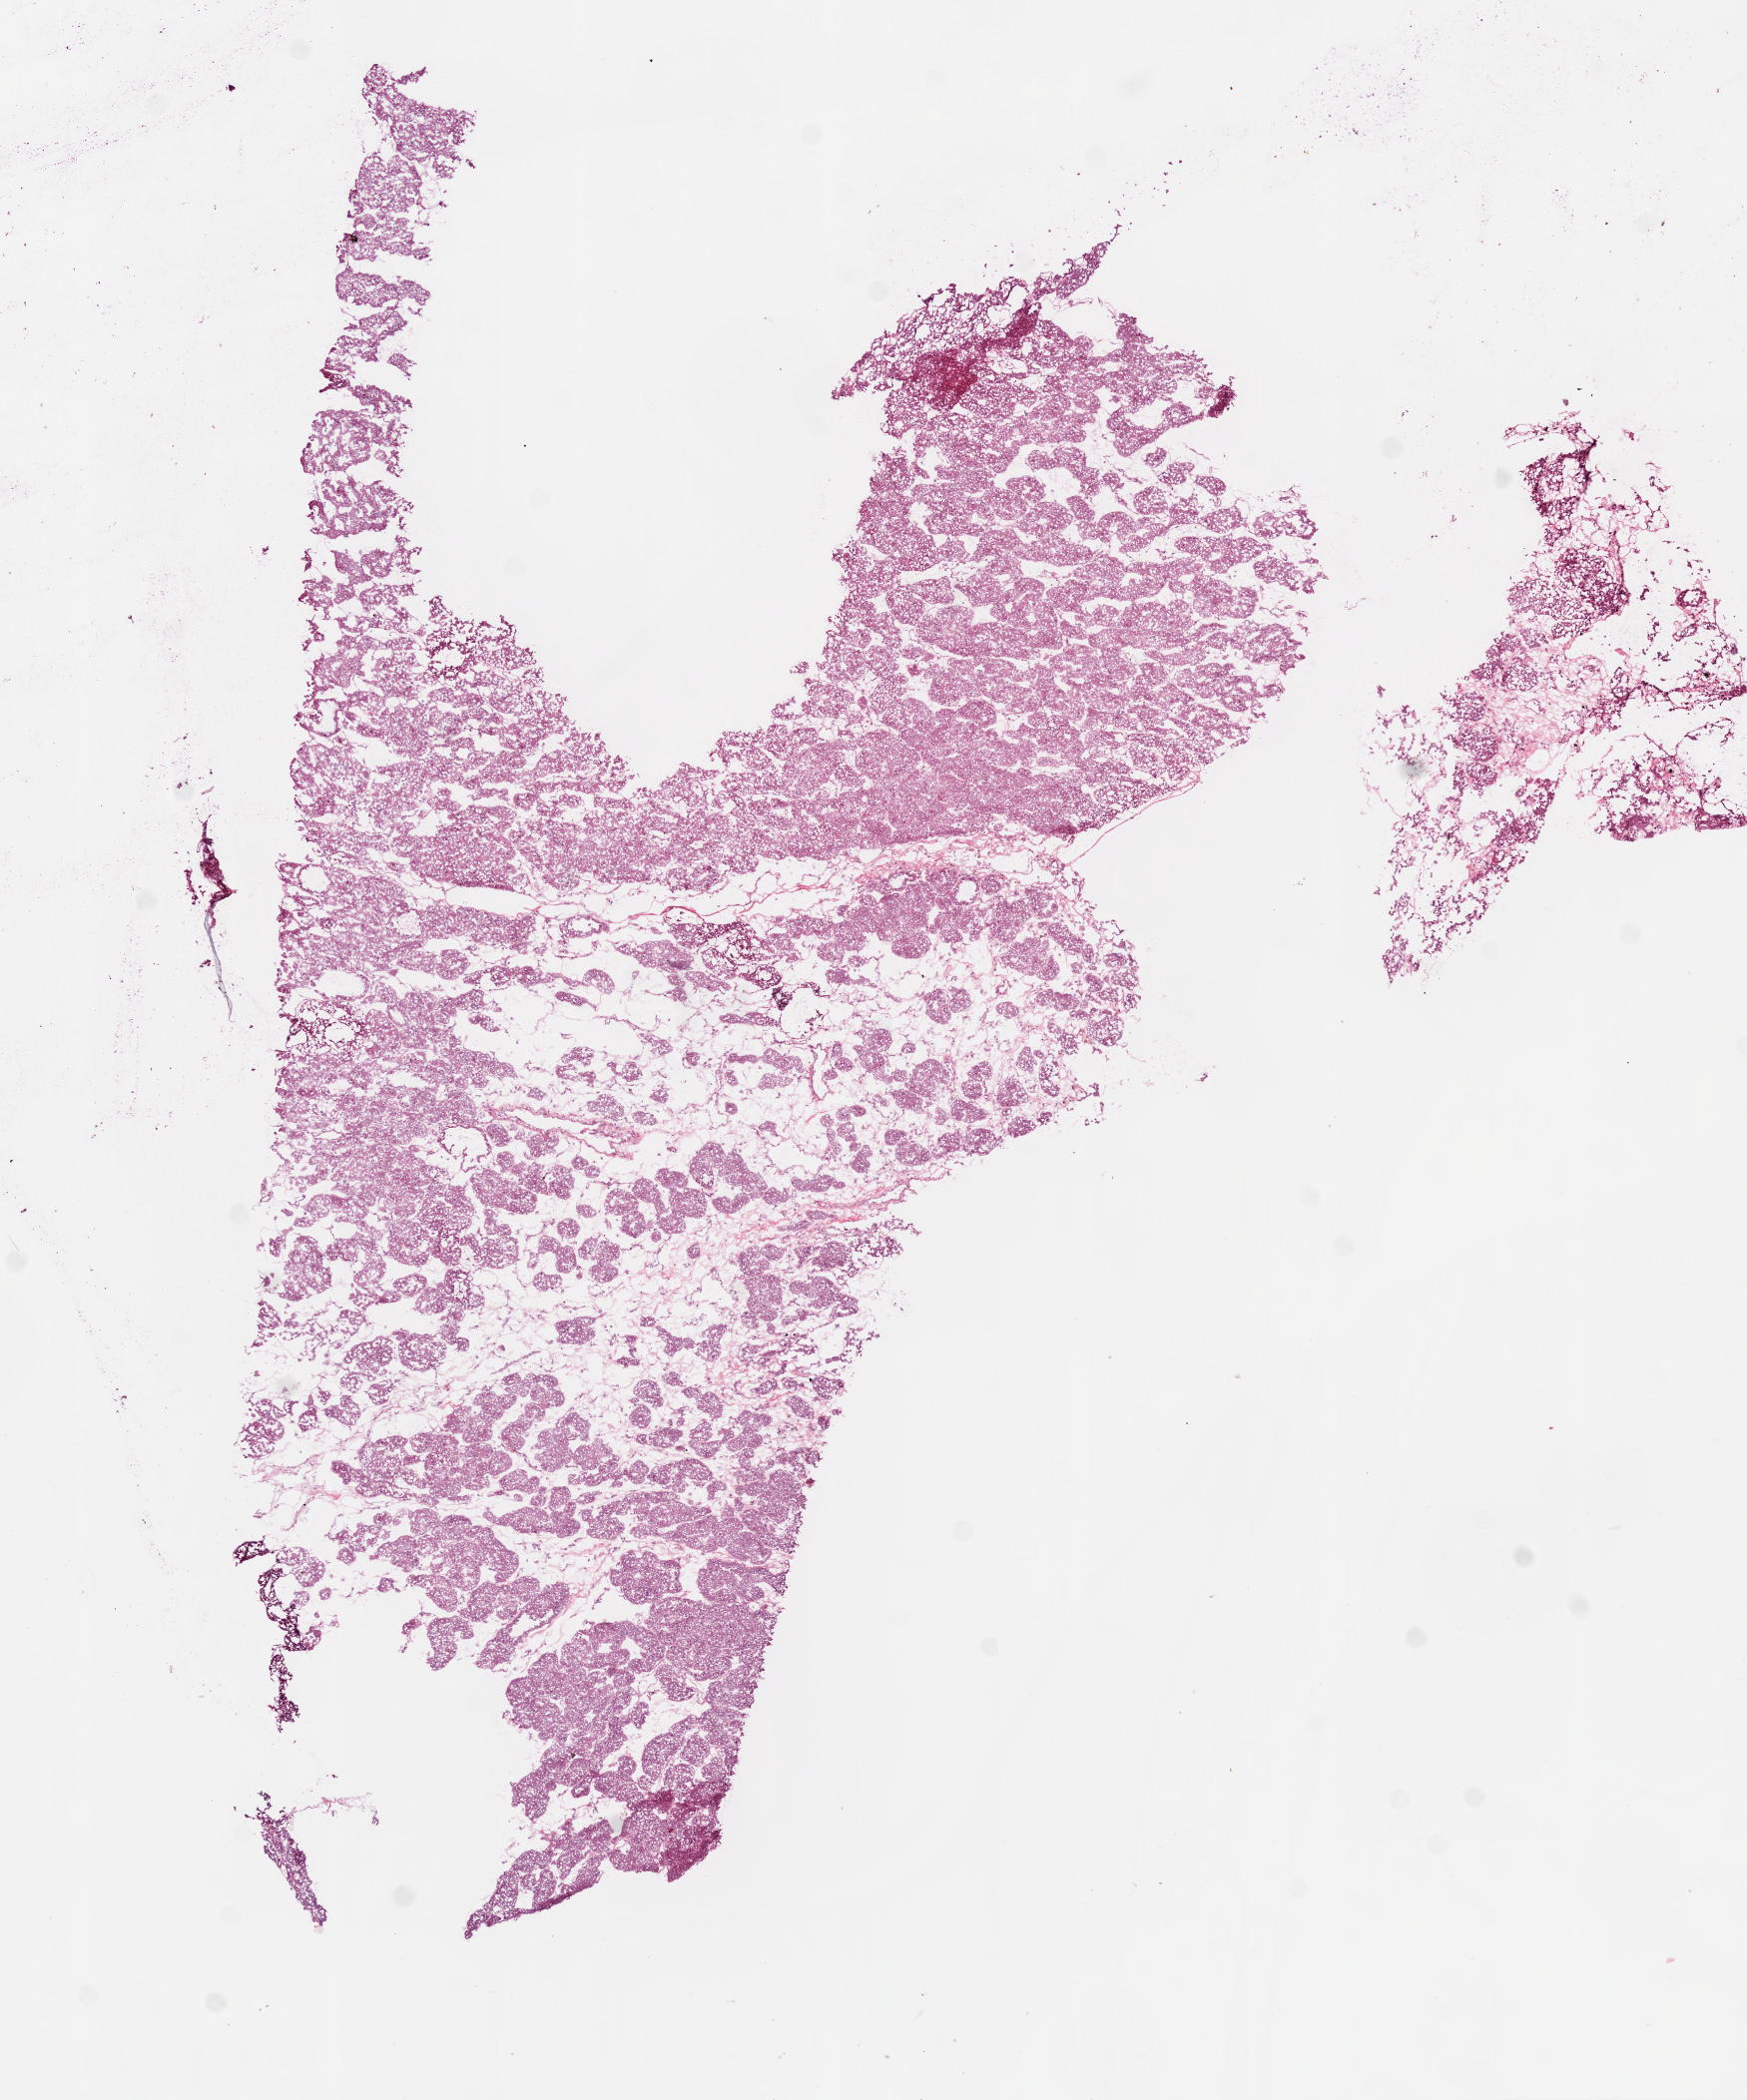
Whole-slide histology image, H&E, a low-resolution overview of the entire scanned area, about 7.0 x 8.4 mm. Frozen section from the bottom of the tissue portion. Kidney, primary tumour sample. Male patient; age at initial diagnosis 58 years. Histologic grade: G2 (moderately differentiated). Pathologist review of this section (percent, as recorded): tumour cells 95%, tumour nuclei 85%, normal cells 0%, stromal cells 5%, necrosis 0%.
AJCC pathologic stage: I (7th edition). Laterality: left. Histologic diagnosis: Clear cell adenocarcinoma, NOS.